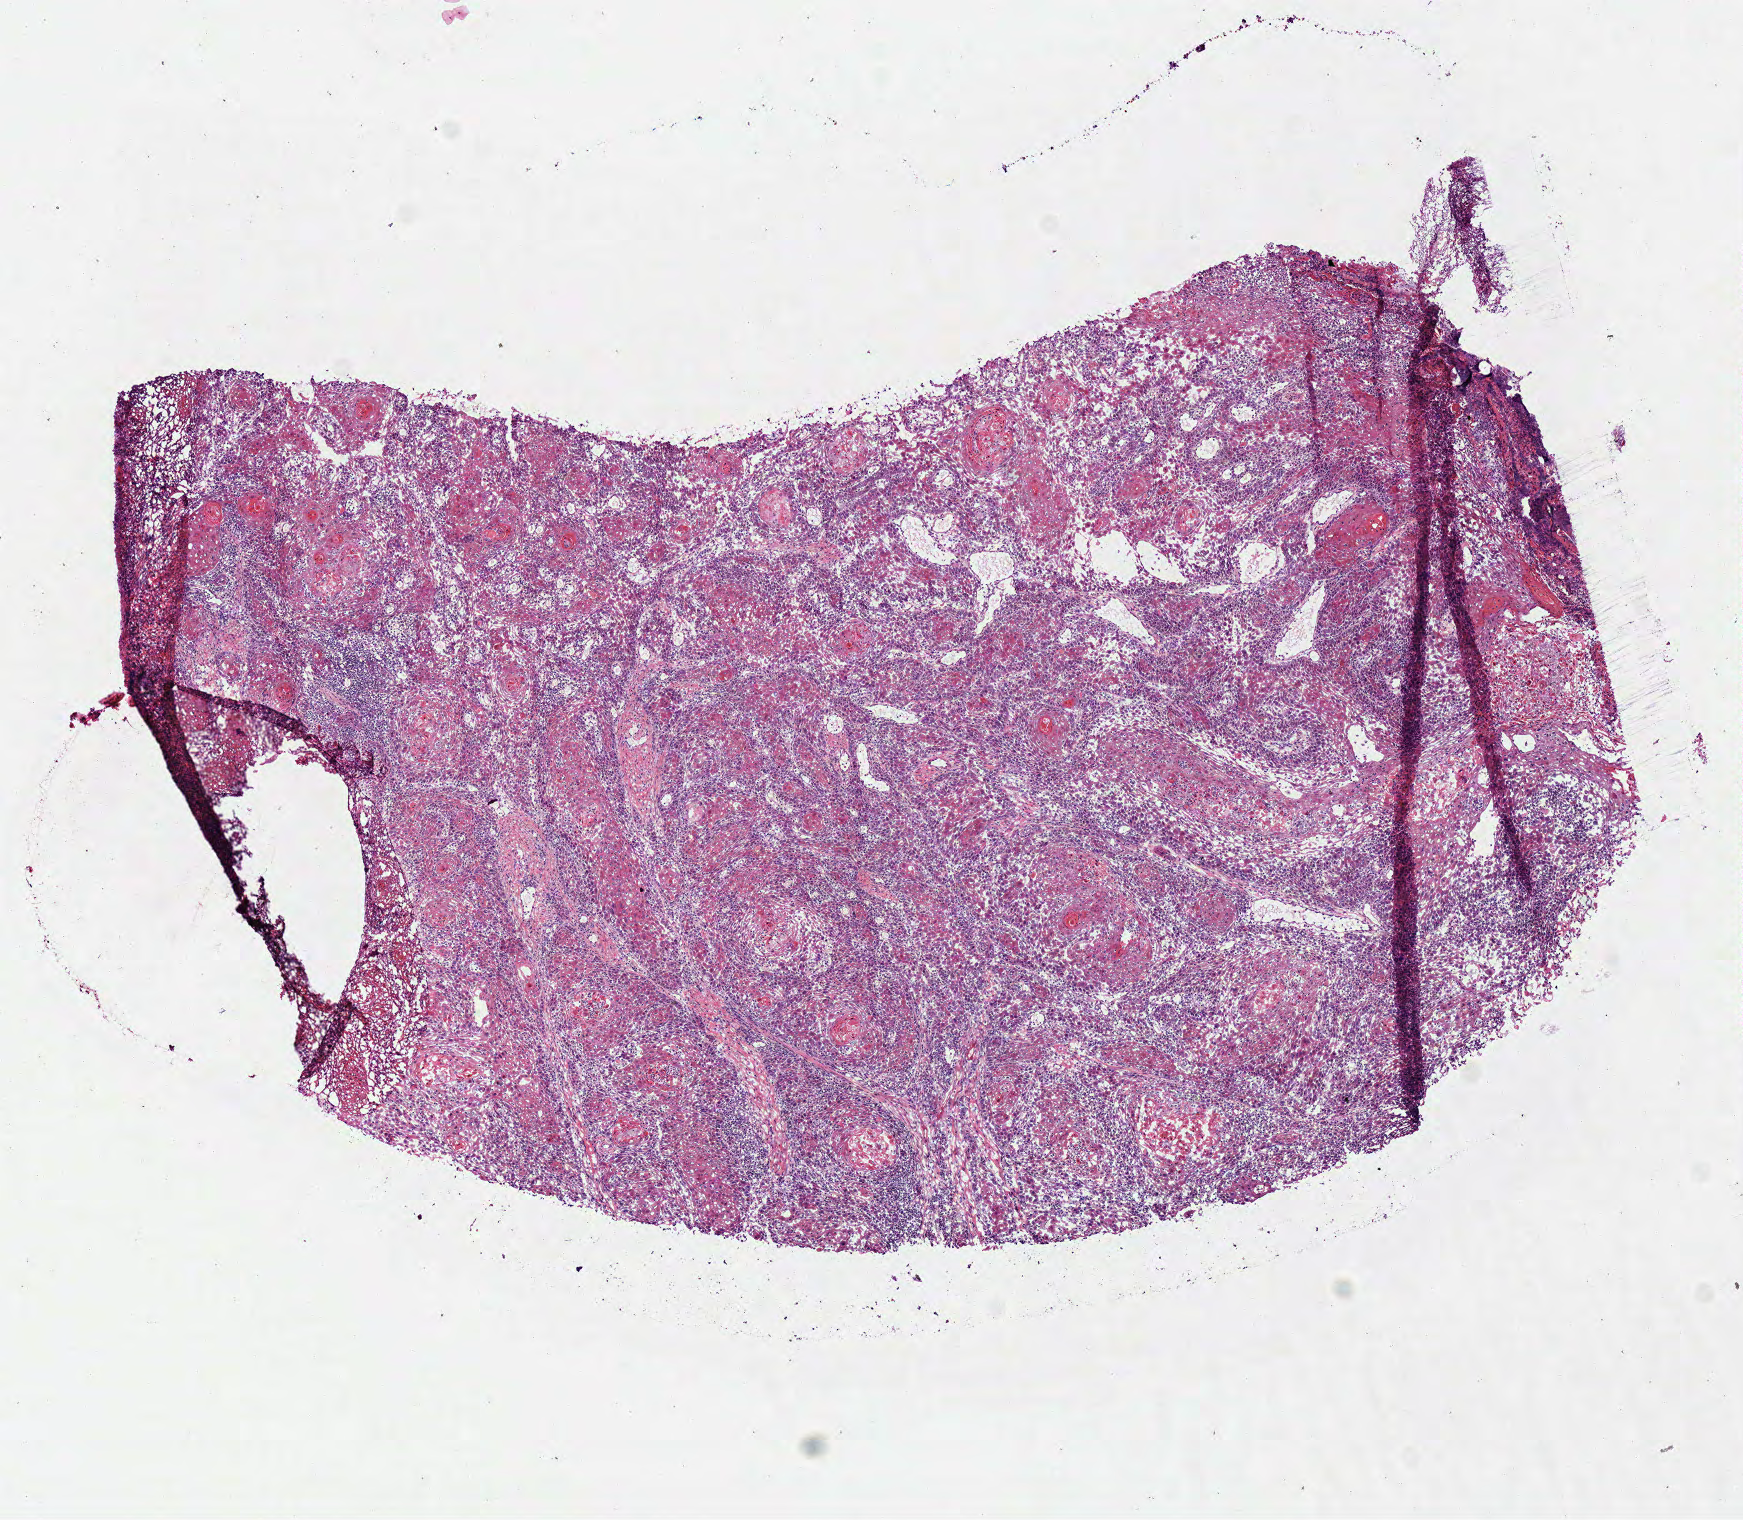
H&E whole-slide image — whole scanned area (about 6.9 x 6.0 mm) shown as a low-resolution overview; frozen section; sample: primary tumour, head and neck. Male, age 69 years at initial diagnosis. Histologic grade: G2 (moderately differentiated). Slide review estimates, as recorded: tumour cells 95%, tumour nuclei 85%, normal cells 0%, stromal cells 5%, necrosis 0%.
Diagnosis: Squamous cell carcinoma, NOS. Laterality: right. AJCC pathologic stage: I. TNM: T1 N0. Lymph nodes positive (case pathology): 0 of 8 examined.